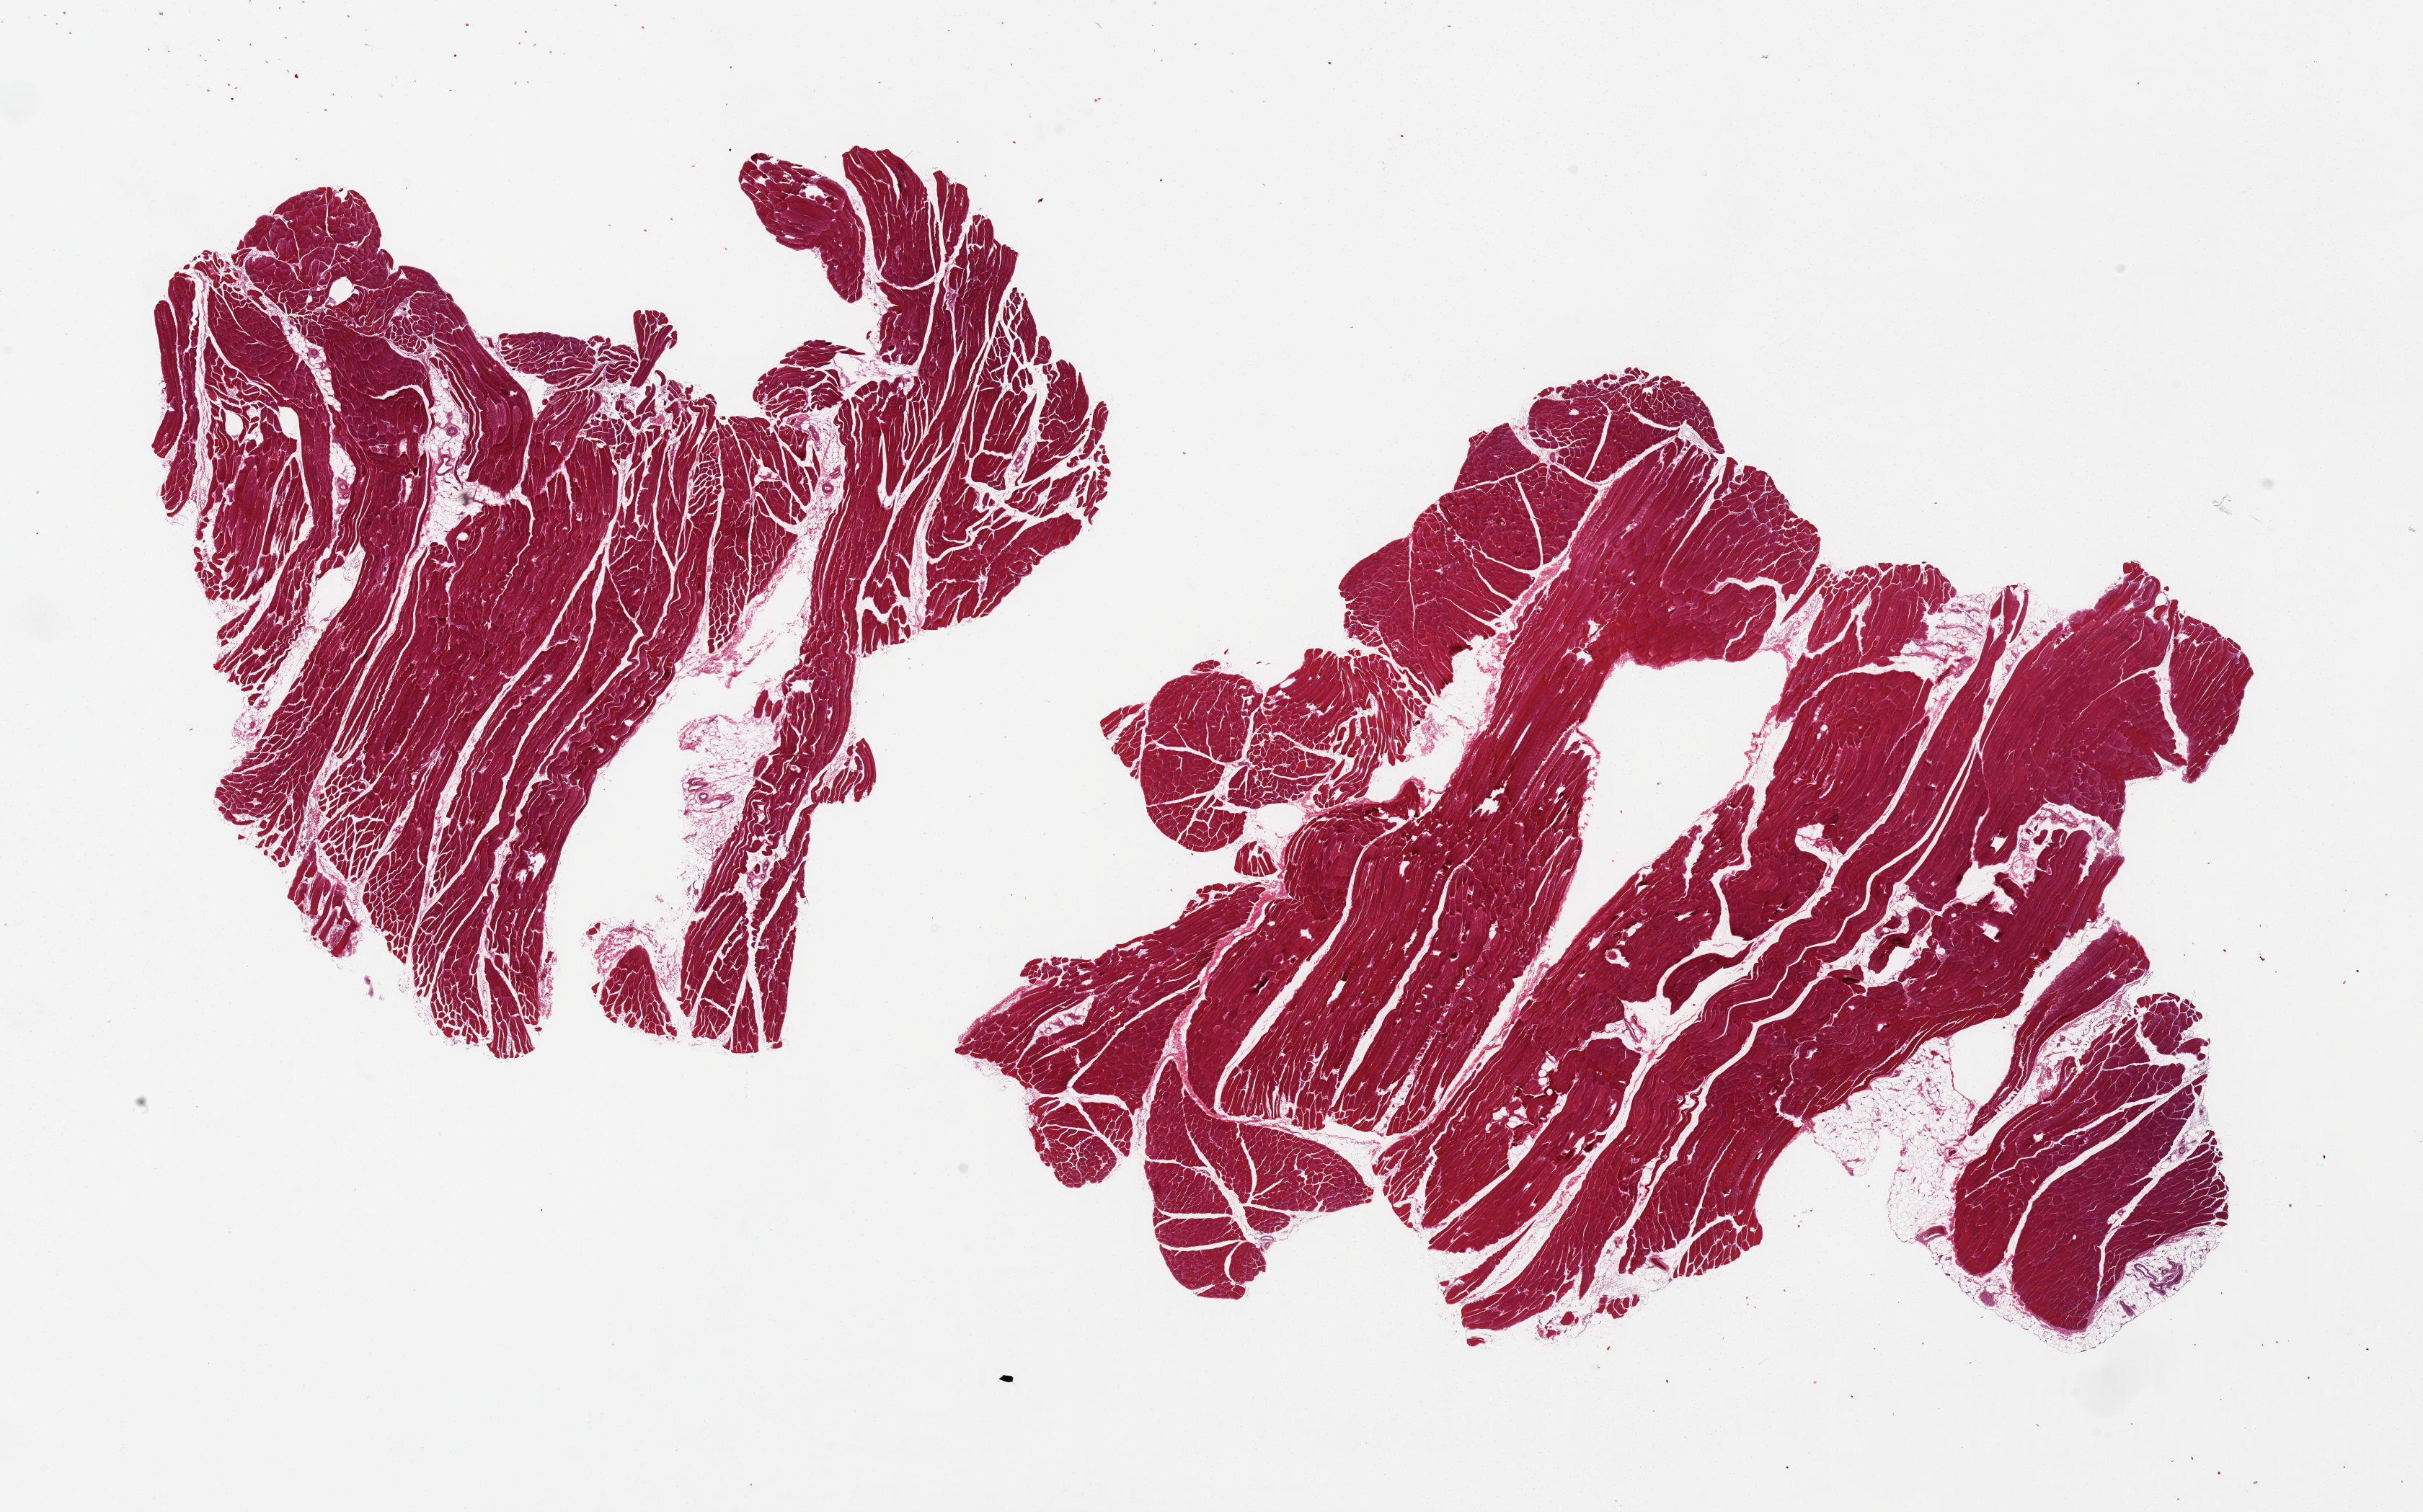
Digitized H&E-stained section — shown as a low-resolution overview of the whole scanned area (about 26.6 x 16.6 mm, slide scanned at 20x); PAXgene-fixed paraffin-embedded (PFPE) section; target tissue: skeletal muscle; tissue donor sample. Male donor.
* reviewer comment on this tissue sample: 2 pieces; <10% adipose tissue (attached and internal)